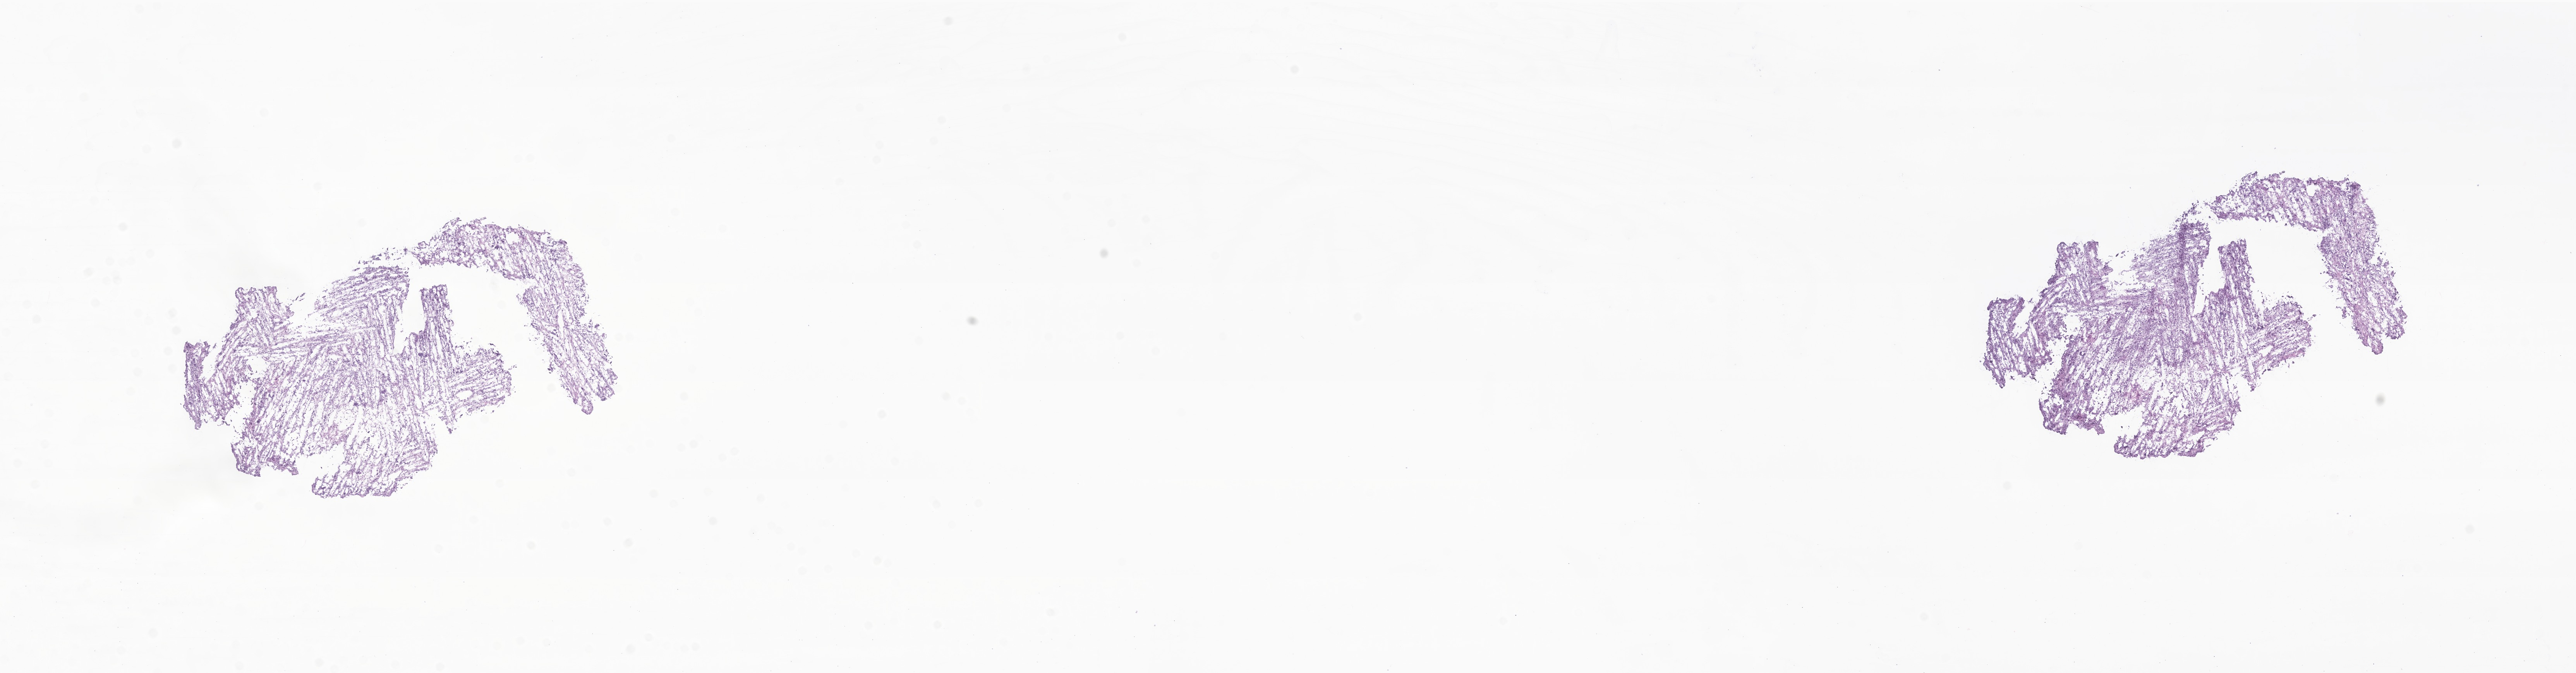
Digitized H&E-stained section of tumor tissue from the soft tissue of pelvis, shown as a low-resolution overview of the whole scanned area (about 28.0 x 7.3 mm). Cryosection (OCT / tissue freezing medium). Female patient, age 34 months (2 years 10 months).
Recorded diagnosis: Embryonal rhabdomyosarcoma, NOS.